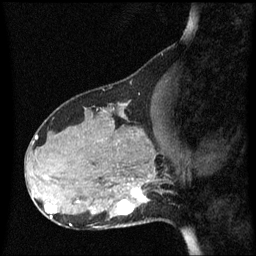
Breast MRI (dynamic contrast-enhanced), one sagittal slice; slice 22 of 60 in the series (ordered by position); dynamic contrast-enhanced series, image 2 of 3 at this slice position (ordered by acquisition); 1.5 T; TE 4.2 ms, TR 8.4 ms; 2.1 mm slice thickness; 256 × 256 image matrix, field of view 210 × 210 mm. Female patient, age 31 years. From the clinical record (not read from this slice): setting: breast cancer imaged before/during neoadjuvant chemotherapy; receptor status: HR-positive, HER2-negative.
Outlined on this slice (semi-automatic segmentation, software-assisted and operator-edited):
- analysis volume of interest (the breast-tissue region the enhancement analysis was run in; not a lesion): bounding box <98,175,165,228> (left, top, right, bottom; pixels)
- tumour enhancement mask (voxels above the 70 % enhancement threshold inside the analysis volume of interest): <119,188,147,216>